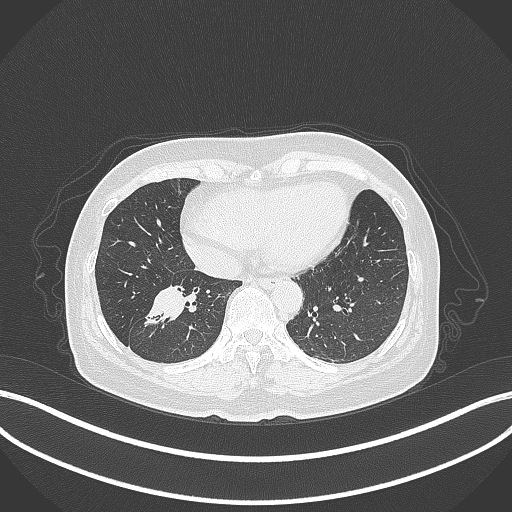
Chest CT, one axial slice. Slice 129 of 429 in the series (ordered by position). Lung window (W 1500 / L -600 HU). 1 mm slice thickness. 512 × 512 image matrix, field of view 400 × 400 mm. Patient: female, 67 years. From the clinical record (not read from this slice): clinical TNM (as recorded): T1c N1 M0; histopathological grade: G2-3.
Annotated regions visible in this slice (bounding box drawn by a radiologist):
- lung tumour (recorded histology: adenocarcinoma): bounding box (x1, y1, x2, y2) in pixels: (136, 283, 193, 335)